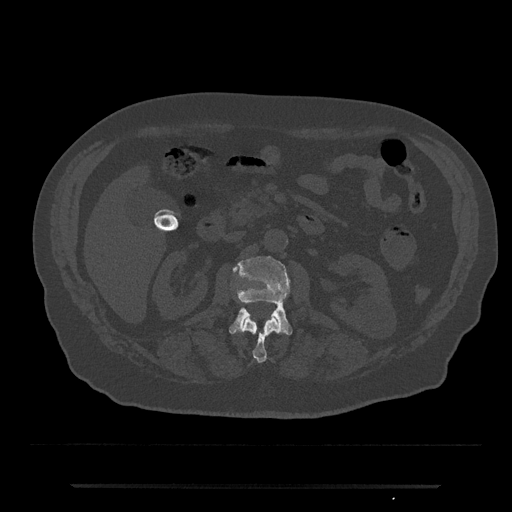
CT including the spine, one axial slice; bone window (W 1800 / L 400 HU); 0.5 mm slice thickness; 512 × 512 image matrix, field of view 434 × 434 mm. Male patient, age 80 years. Case-level facts recorded for this patient, not image findings: primary cancer: prostate; vertebrae with lytic lesions (as recorded): L1, T11.
Annotated regions visible in this slice (semi-automatically segmented with operator editing):
- L1 vertebra: box from (x=243, y=317) to (x=280, y=363) px
- L2 vertebra: (x=229, y=256)–(x=293, y=335)